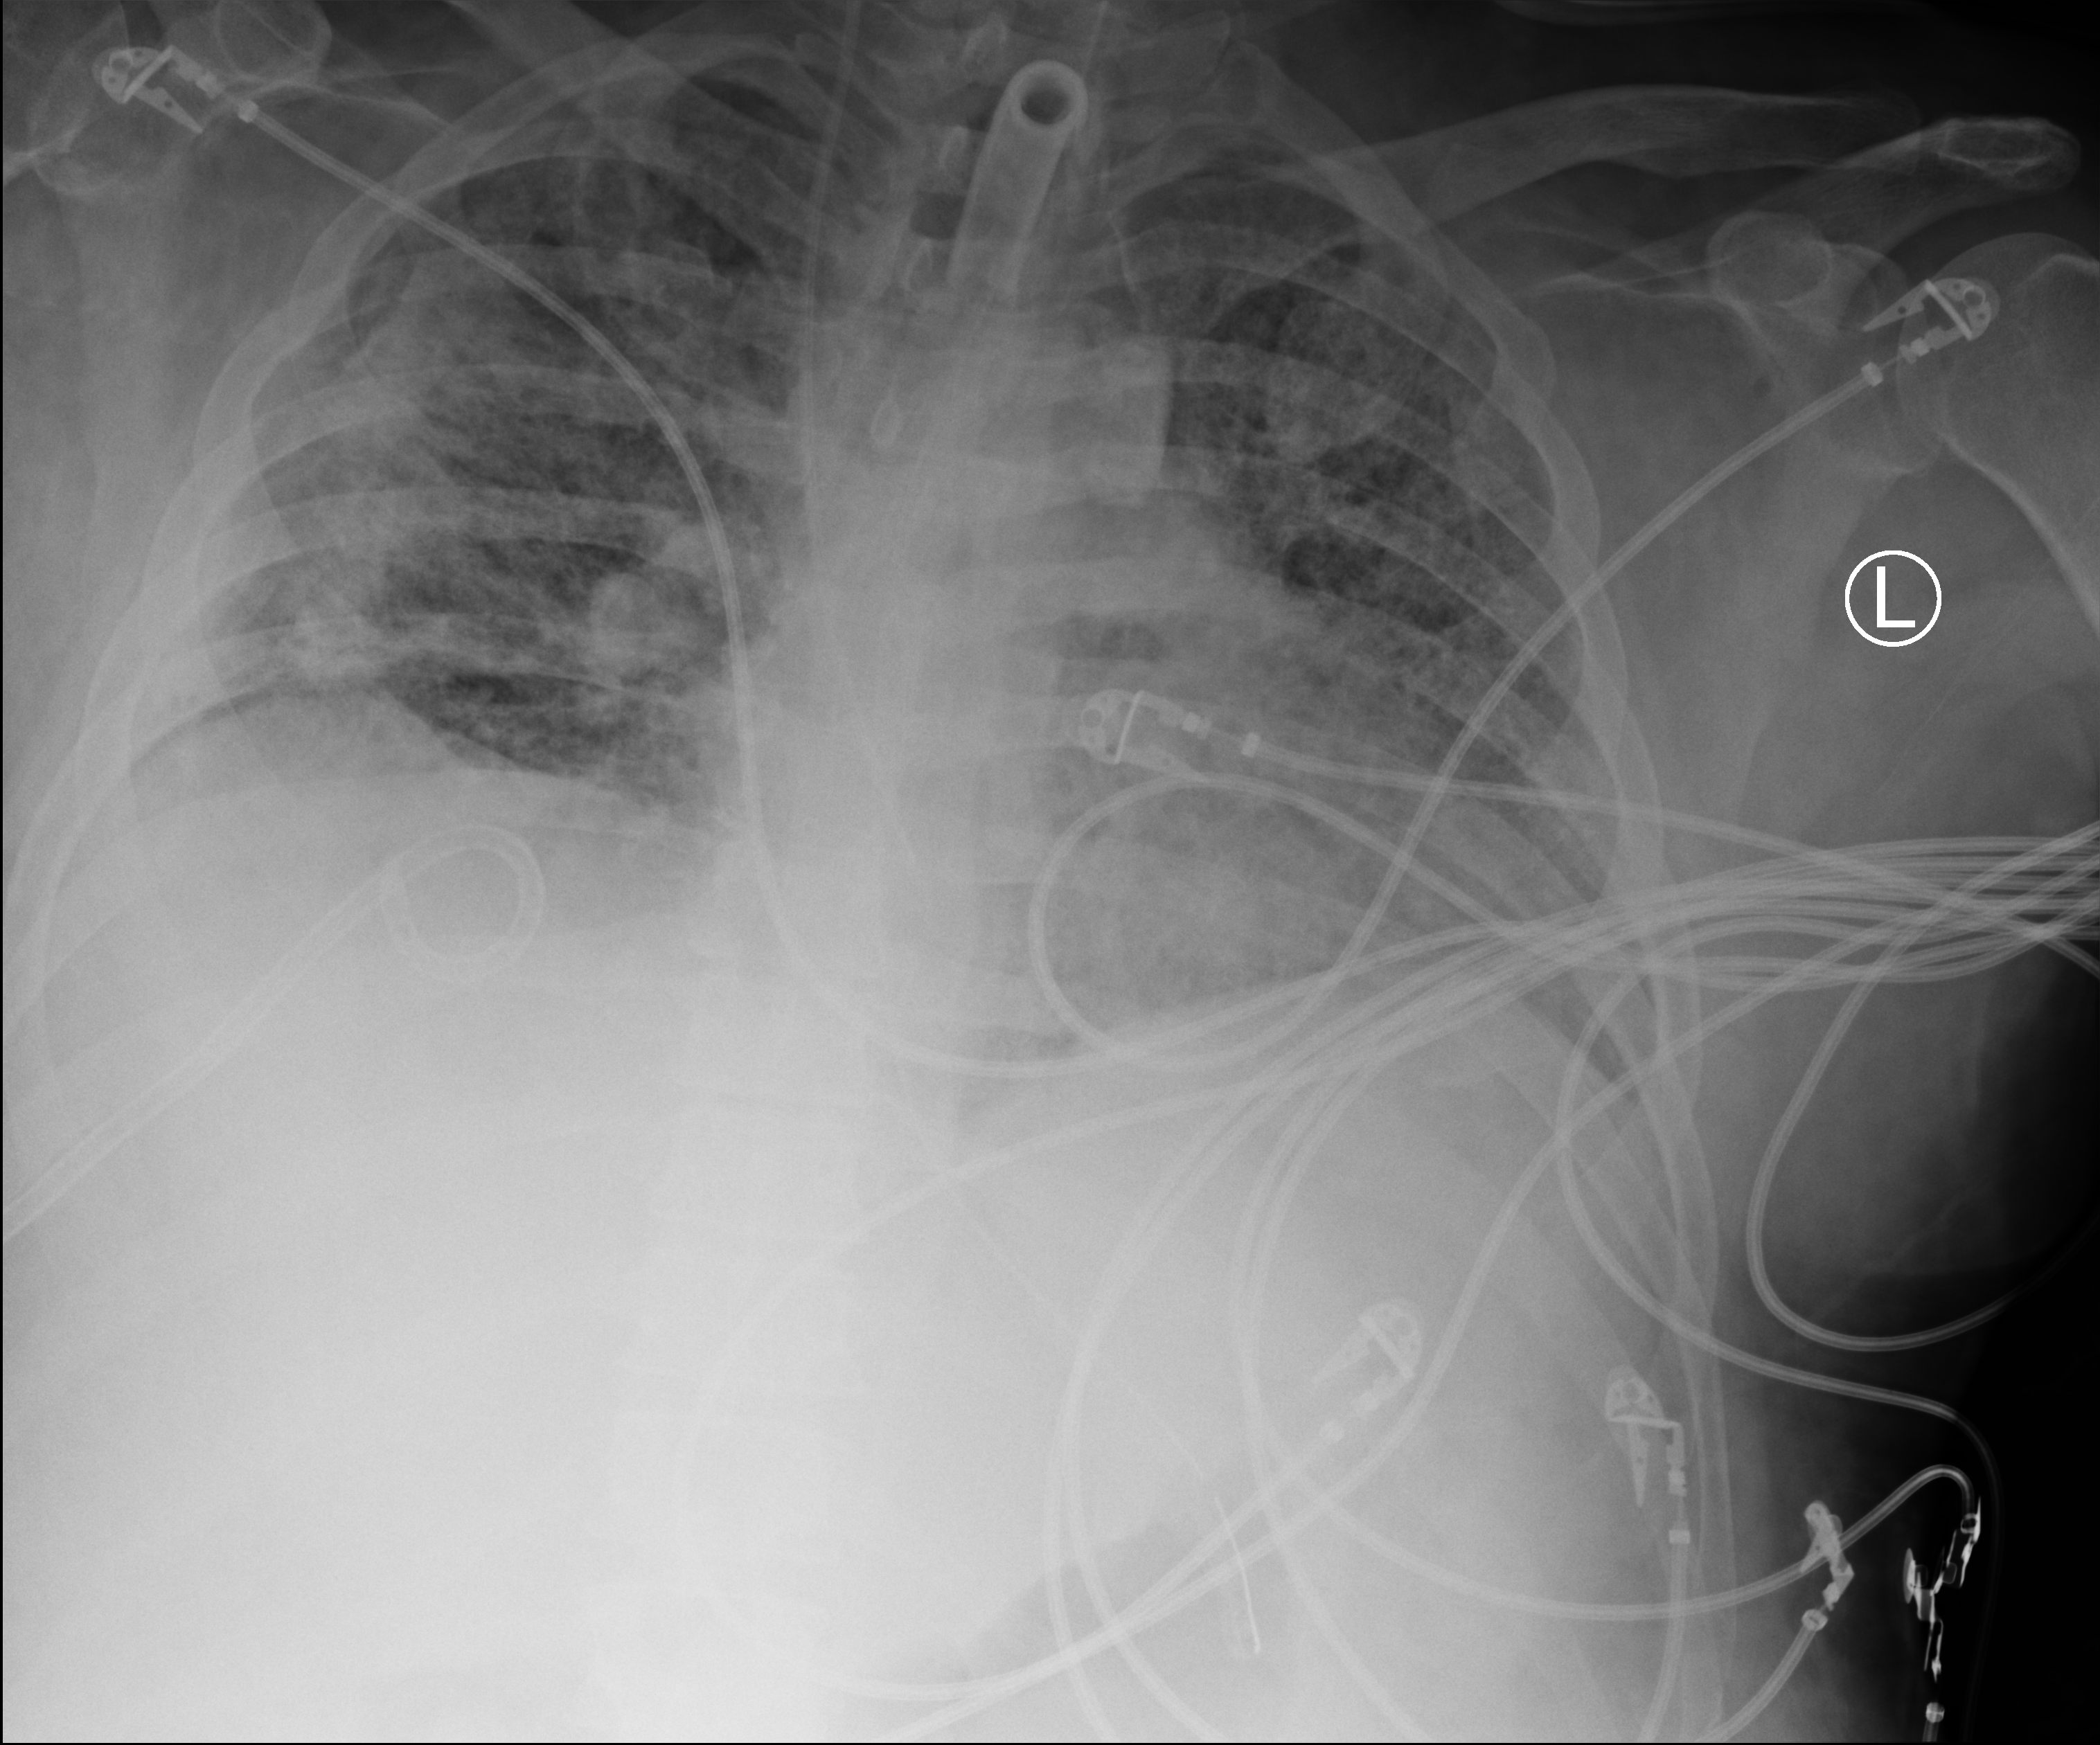
Bedside chest radiograph (computed radiography), anteroposterior (AP) projection. Patient hospitalised with COVID-19; male, aged 18–59 years.
Admission-level facts for this patient (not findings on this image; timing relative to this image not recorded): admitted to intensive care during this hospital stay: yes; smoking status (admission record): never.